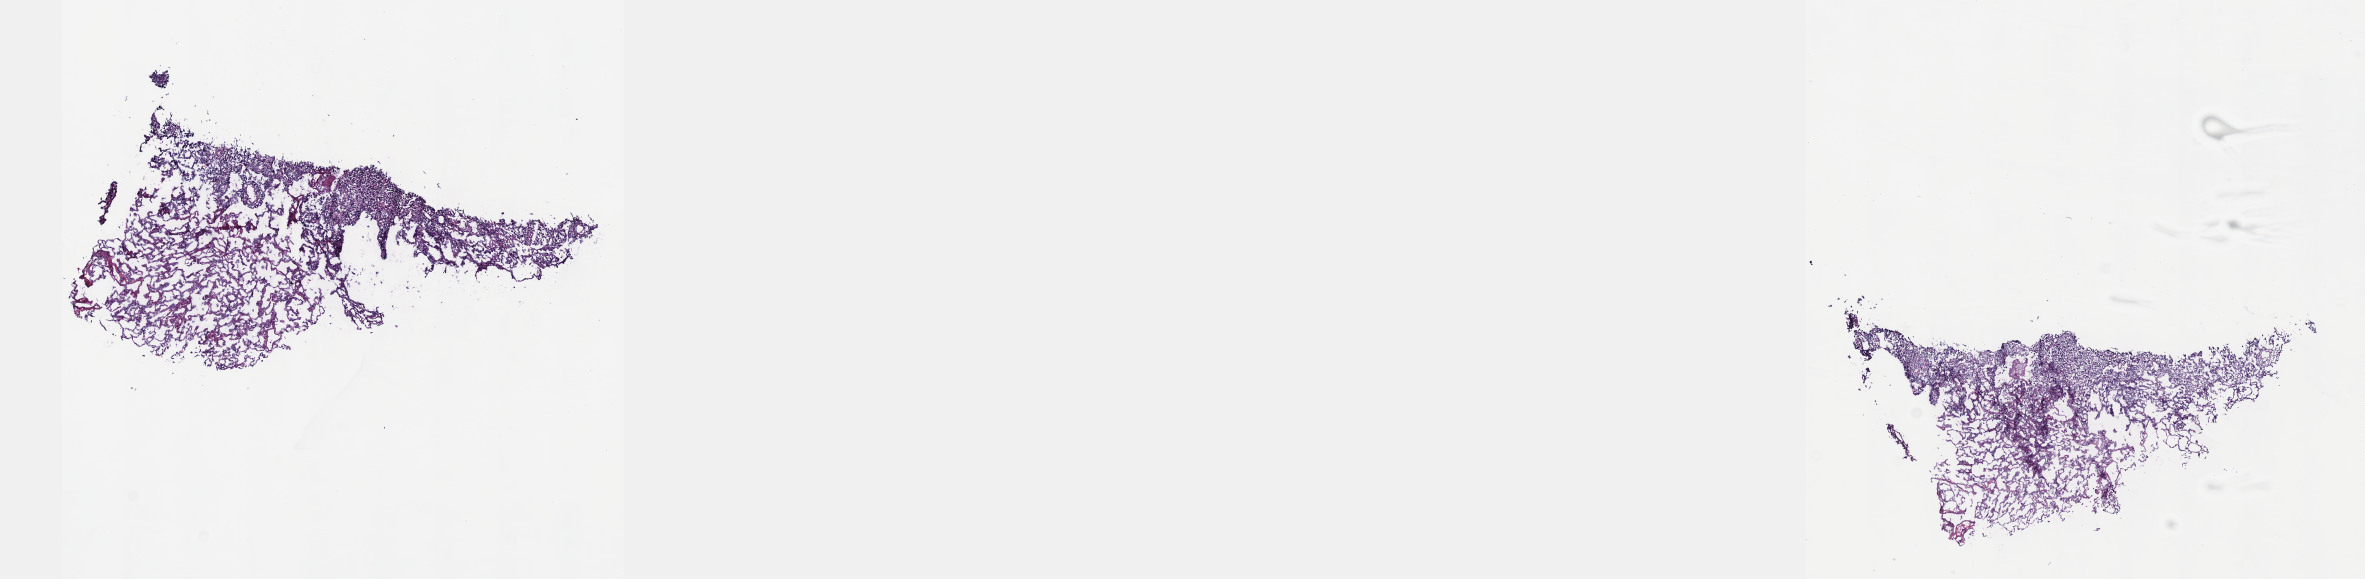
Digitized H&E-stained tissue section (whole slide), a low-resolution overview of the entire scanned area, about 19.1 x 4.7 mm (slide scanned at 40x); frozen section from the top of the tissue portion; metastatic tumour sample. Male, age 29 years at initial diagnosis. Composition of this section per pathologist review: tumour cells 70%, tumour nuclei 100%, normal cells 0%, stromal cells 25%, necrosis 5%. Inflammatory infiltration, as recorded: lymphocyte infiltration 0%, monocyte infiltration 0%, neutrophil infiltration 0%.
This section: metastatic tumour tissue. Patient diagnosis: Malignant peripheral nerve sheath tumor (primary site: connective, subcutaneous and other soft tissues of lower limb and hip).